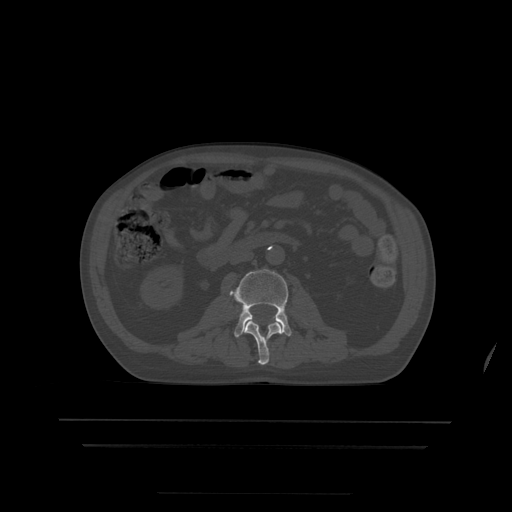
CT including the spine, one axial slice. Position 130 of 522 along the scan axis. Bone window (W 1800 / L 400 HU). 1.25 mm slice thickness. 512 × 512 image matrix. Patient age 68 years. Case-level facts recorded for this patient, not image findings: primary cancer: urothelial.
Outlined on this slice (semi-automatically segmented with operator editing):
- L2 vertebra: bounding box [x1, y1, x2, y2] px = [245, 320, 282, 365]
- L3 vertebra: [230, 269, 292, 338]